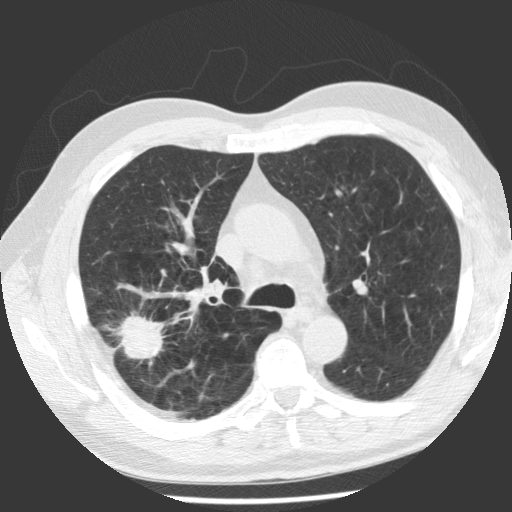
Low-dose screening chest CT, one axial slice. 140 kVp. Lung window (W 1500 / L -600 HU). 2.5 mm slice thickness. 512 × 512 image matrix, field of view 344 × 344 mm.
Structures marked on this image (manually delineated by an expert):
- lesion 1 (tumor, upper lobe of right lung): box from (x=120, y=314) to (x=165, y=360) px